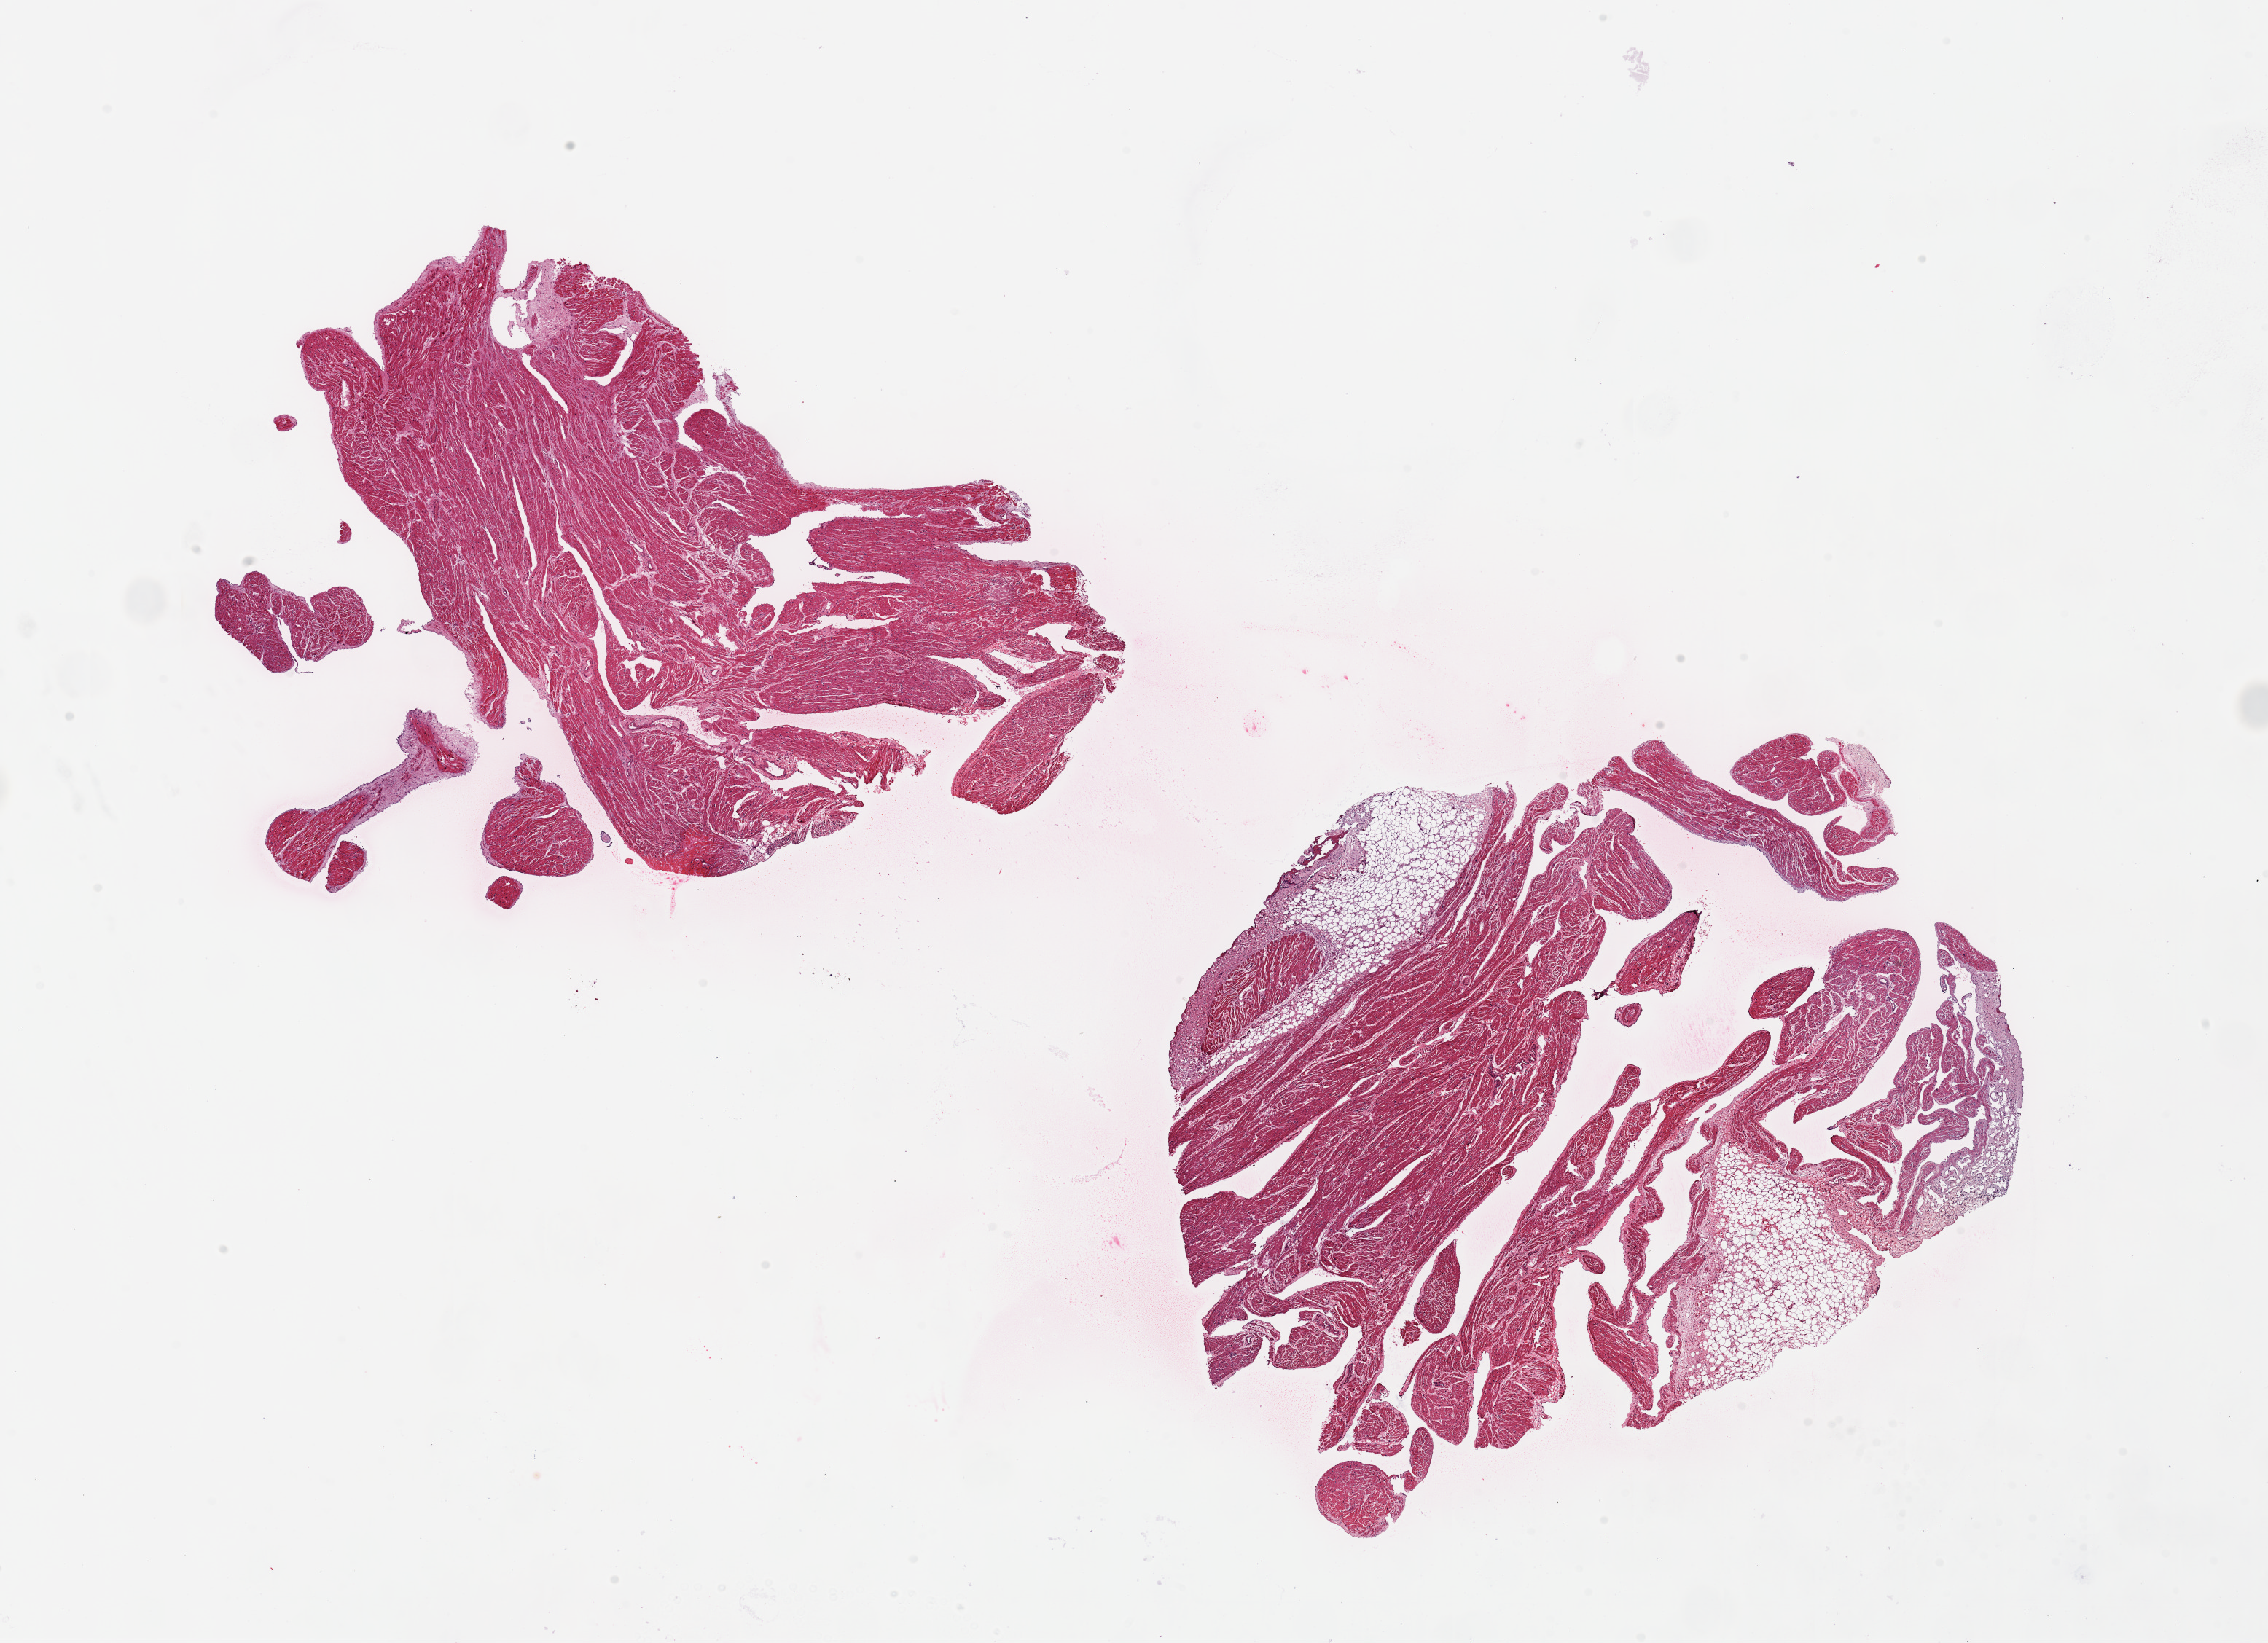
Whole-slide image, H&E stain — shown as a low-resolution overview of the whole scanned area (about 24.6 x 17.8 mm, from a 20x scan); PAXgene-fixed, paraffin-embedded tissue; target tissue: auricular appendage; donor tissue sample. Donor: male.
Reviewer comment on this tissue sample: 2 pieces ~8x6.